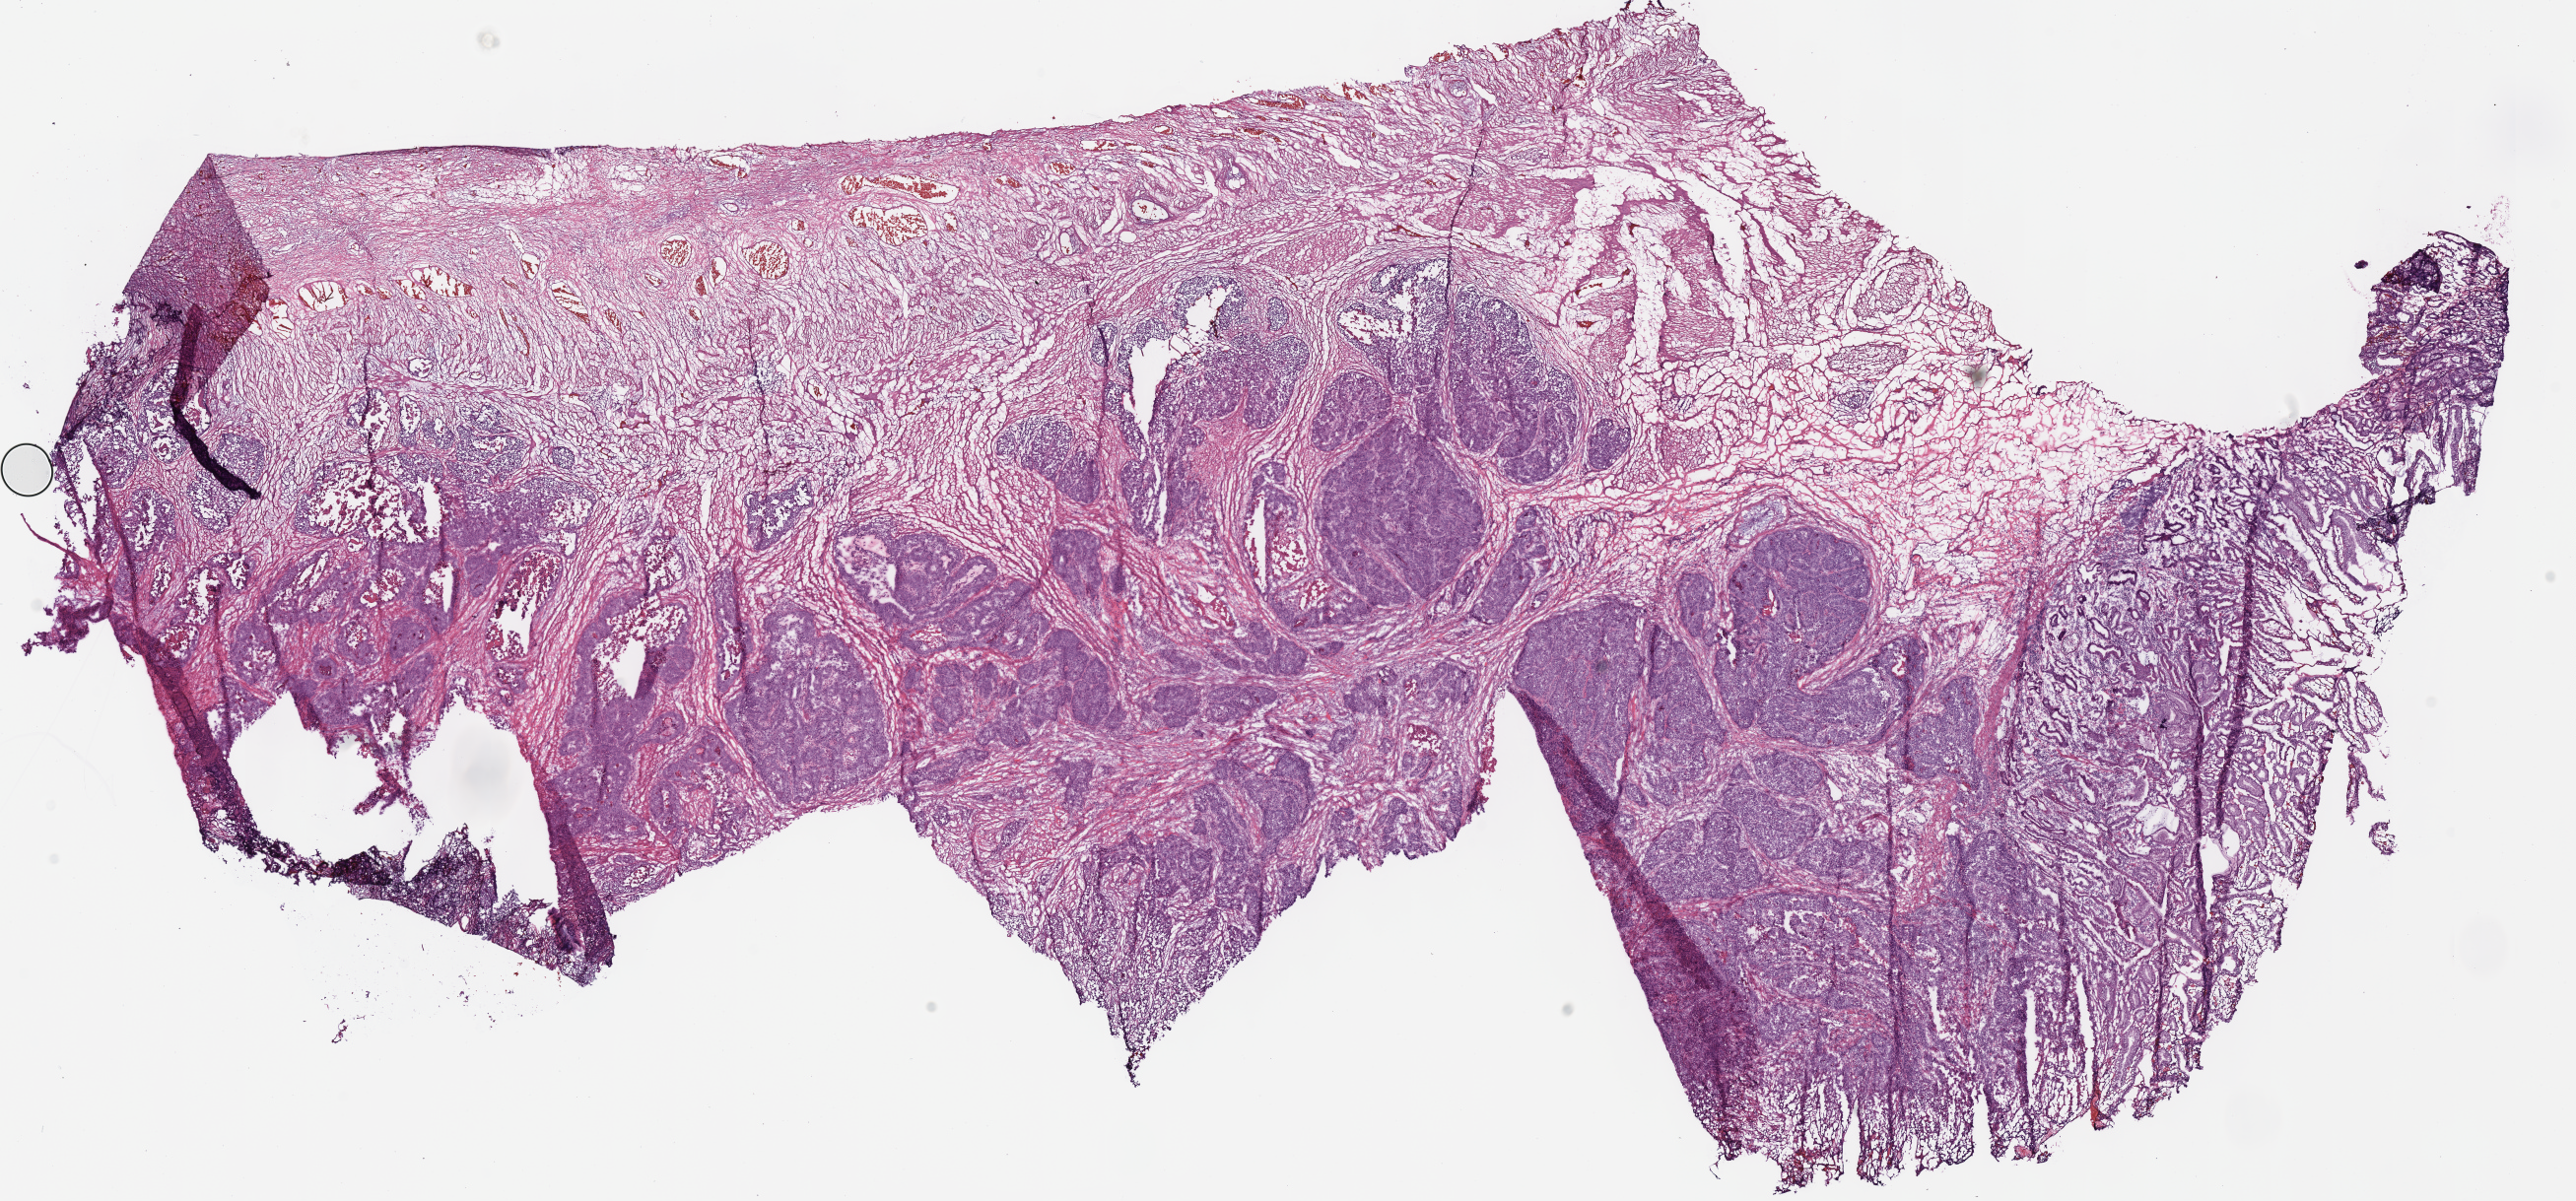
Whole-slide histology image, H&E-stained, a low-resolution overview of the entire scanned area, about 20.6 x 9.6 mm (acquisition: 40x scan). Frozen section. Primary tumour sample from the stomach. Male patient; age at initial diagnosis 65 years. Histologic grade: G2 (moderately differentiated). Composition of this section per pathologist review: tumour cells 65%, tumour nuclei 70%, normal cells 5%, stromal cells 25%, necrosis 5%. Infiltration values recorded for this section: lymphocyte infiltration 2%, monocyte infiltration 0%, neutrophil infiltration 0%.
- AJCC pathologic stage: IIA (7th edition)
- lymph nodes positive (case pathology): 0 of 9 examined
- histologic diagnosis: Adenocarcinoma, NOS (body of stomach)